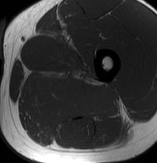
MRI of an extremity soft-tissue mass, one axial slice. Slice 47 of 70 in the series (ordered by position). MR volume resampled by the dataset authors to the PET/CT grid (not the native acquisition matrix). 157 × 163 image matrix, field of view 153 × 159 mm. Male patient. Case-level facts recorded for this patient, not image findings: histological type: extraskeletal osteosarcoma; grade: high; site of the primary tumour: left adductur.
Annotated regions visible in this slice (expert contour drawn on MRI and transferred to this co-registered scan by the dataset authors):
- gross tumour volume (mass): bounding box [x1, y1, x2, y2] px = [31, 65, 121, 123]